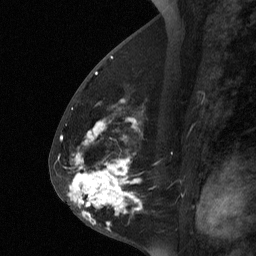
Breast MRI (dynamic contrast-enhanced), one sagittal slice. Slice 31 of 64 in the series (ordered by position). Dynamic contrast-enhanced study with each time point stored as its own series, time point 2 of 3 at this slice position (early post-contrast, ordered by acquisition time). 1.5 T. TE 4.8 ms, TR 27 ms. 2 mm slice thickness. 256 × 256 image matrix. Patient: female, 56 years. Case-level facts recorded for this patient, not image findings: setting: breast cancer imaged before/during neoadjuvant chemotherapy; receptor status: HER2-positive.
Outlined on this slice (semi-automatic segmentation, software-assisted and operator-edited):
- analysis volume of interest (the breast-tissue region the enhancement analysis was run in; not a lesion): bounding box <59,105,143,229> (left, top, right, bottom; pixels)
- tumour enhancement mask (voxels above the 90 % enhancement threshold inside the analysis volume of interest): <69,160,136,224>